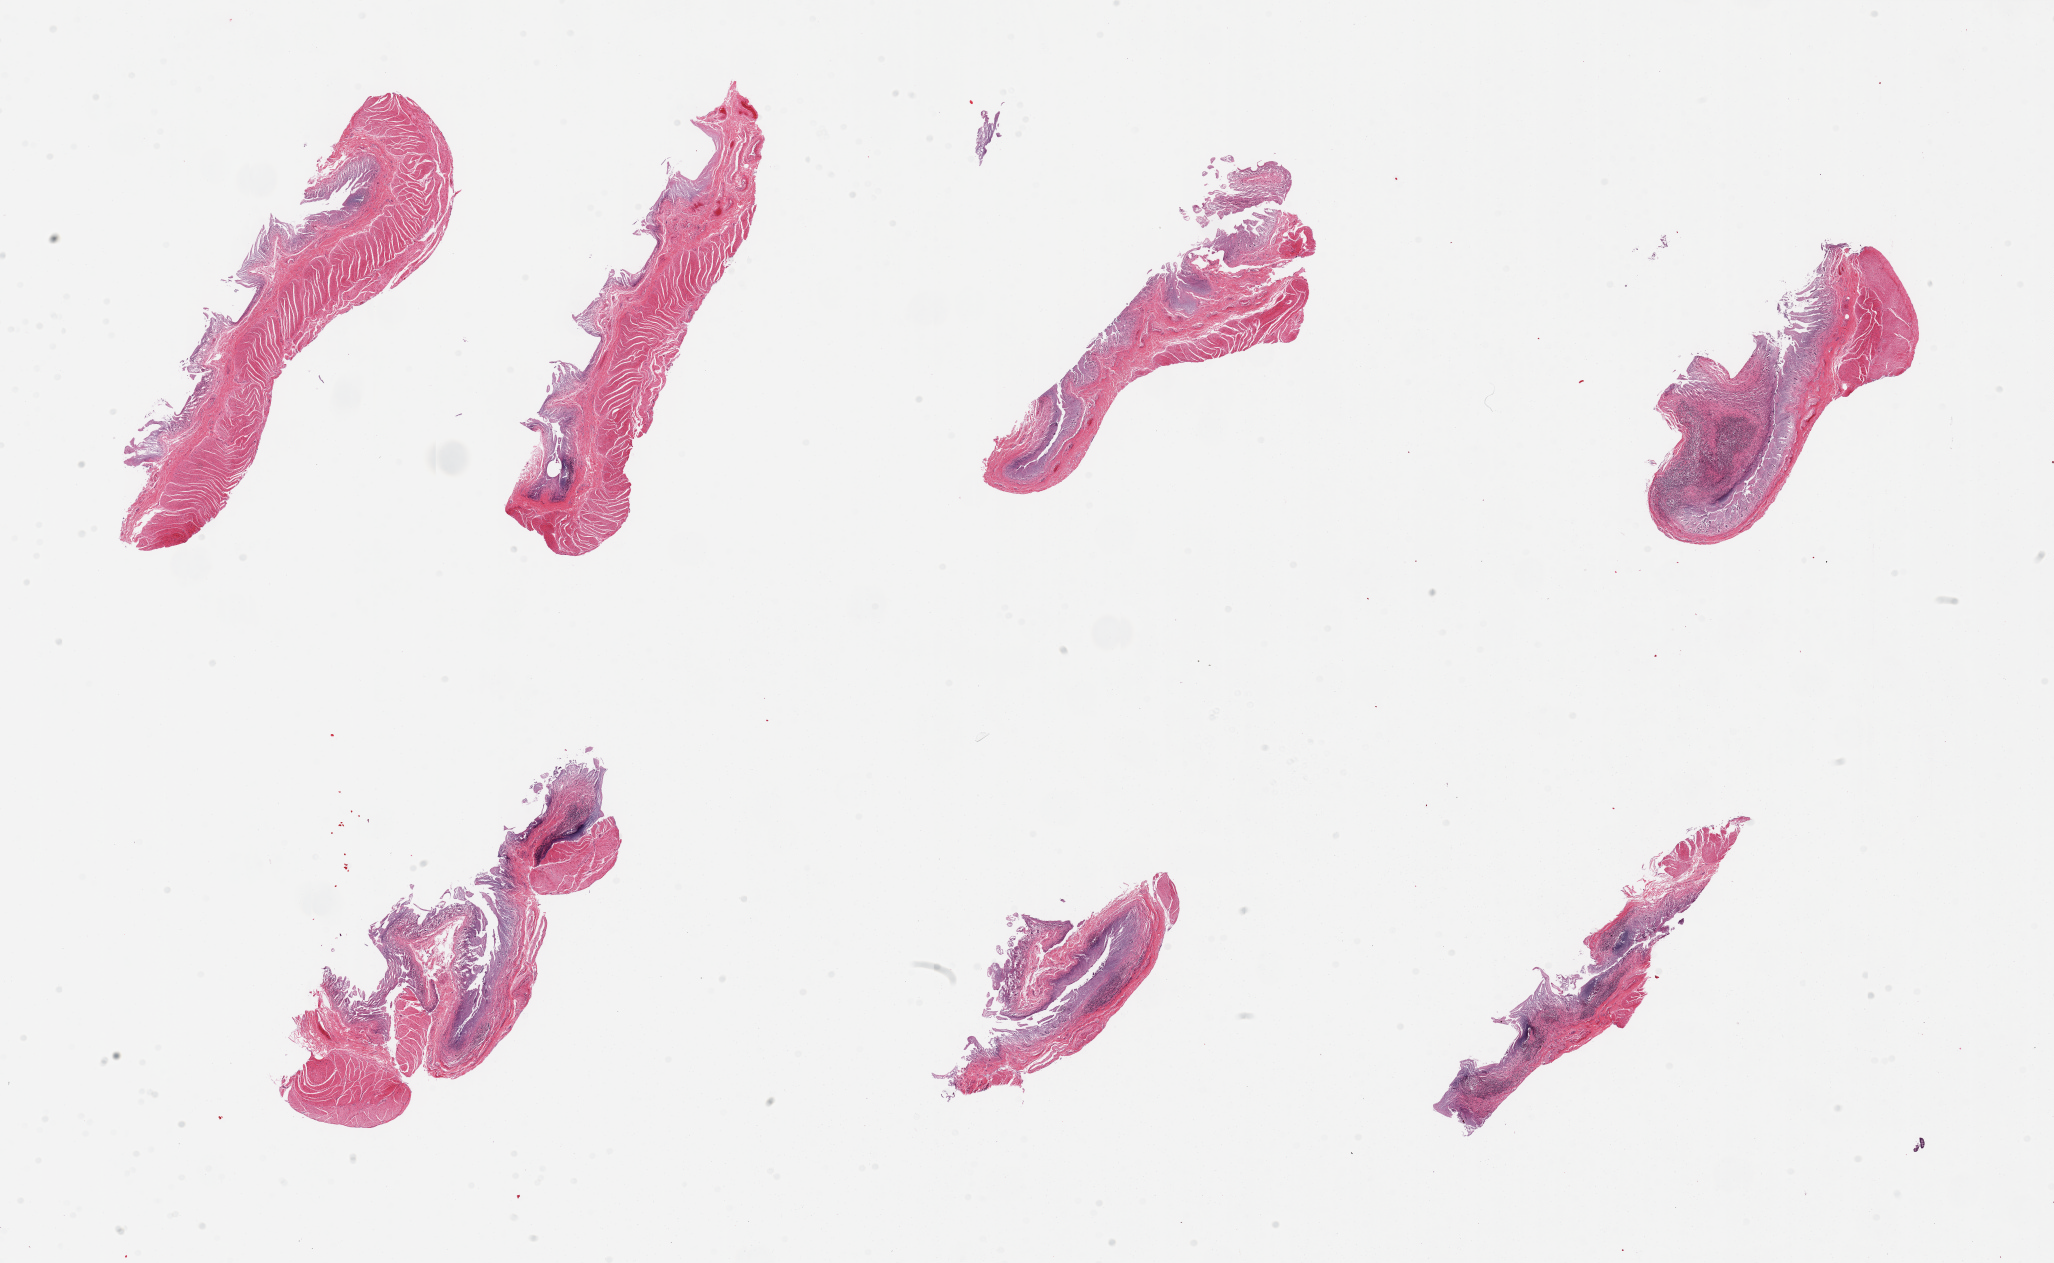
Whole-slide image, H&E stain, shown as a low-resolution overview of the whole scanned area (about 32.5 x 20.0 mm, acquisition: 20x scan); PAXgene-fixed, paraffin-embedded tissue; target tissue: ileum; donor tissue sample.
Reviewer comment on this tissue sample: 6 pieces, mucosa autolyzed, lymphoid aggreates ~10% total tissue.